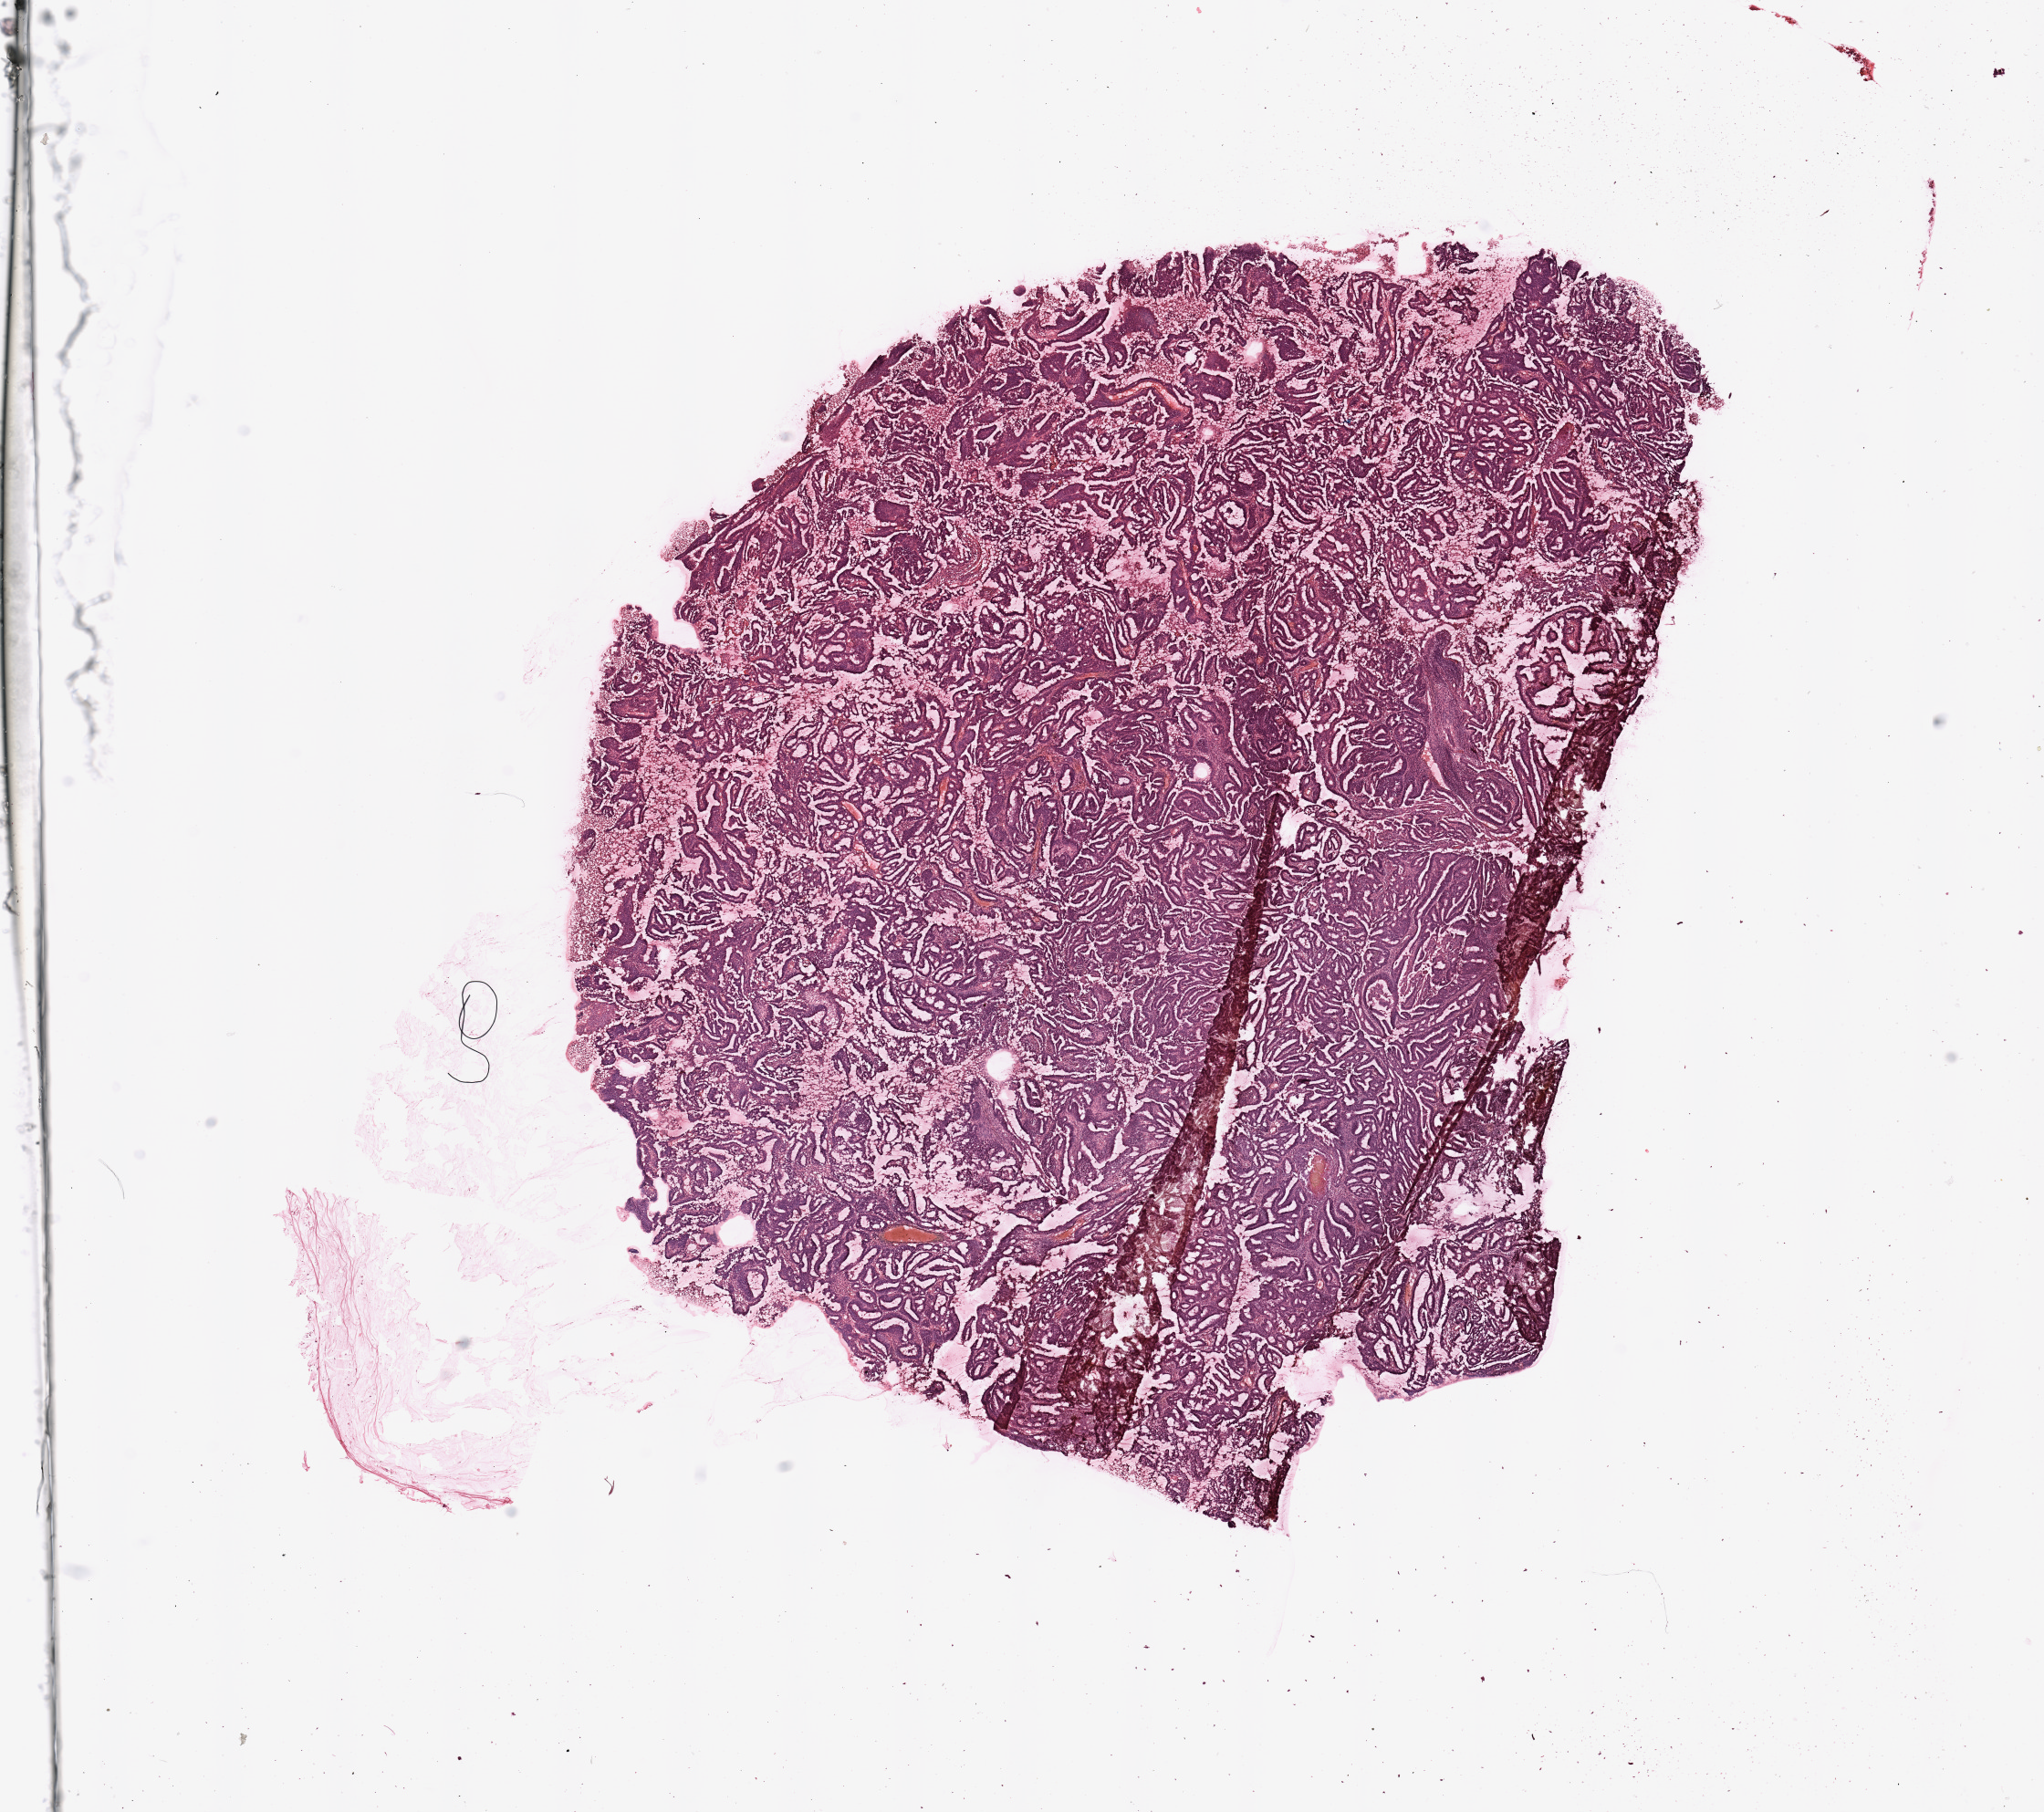
H&E-stained whole-slide image, low-resolution overview of the scanned area, about 17.7 x 15.7 mm (acquisition: 20x scan). Tumour tissue sample, sampled site: uterus. 65-year-old female patient. Histologic grade: G2 (moderately differentiated). Pathologist review of this section (percent, as recorded): tumour nuclei 80%, necrosis 0%.
• AJCC pathologic stage: III
• histologic diagnosis: Endometrioid adenocarcinoma, NOS